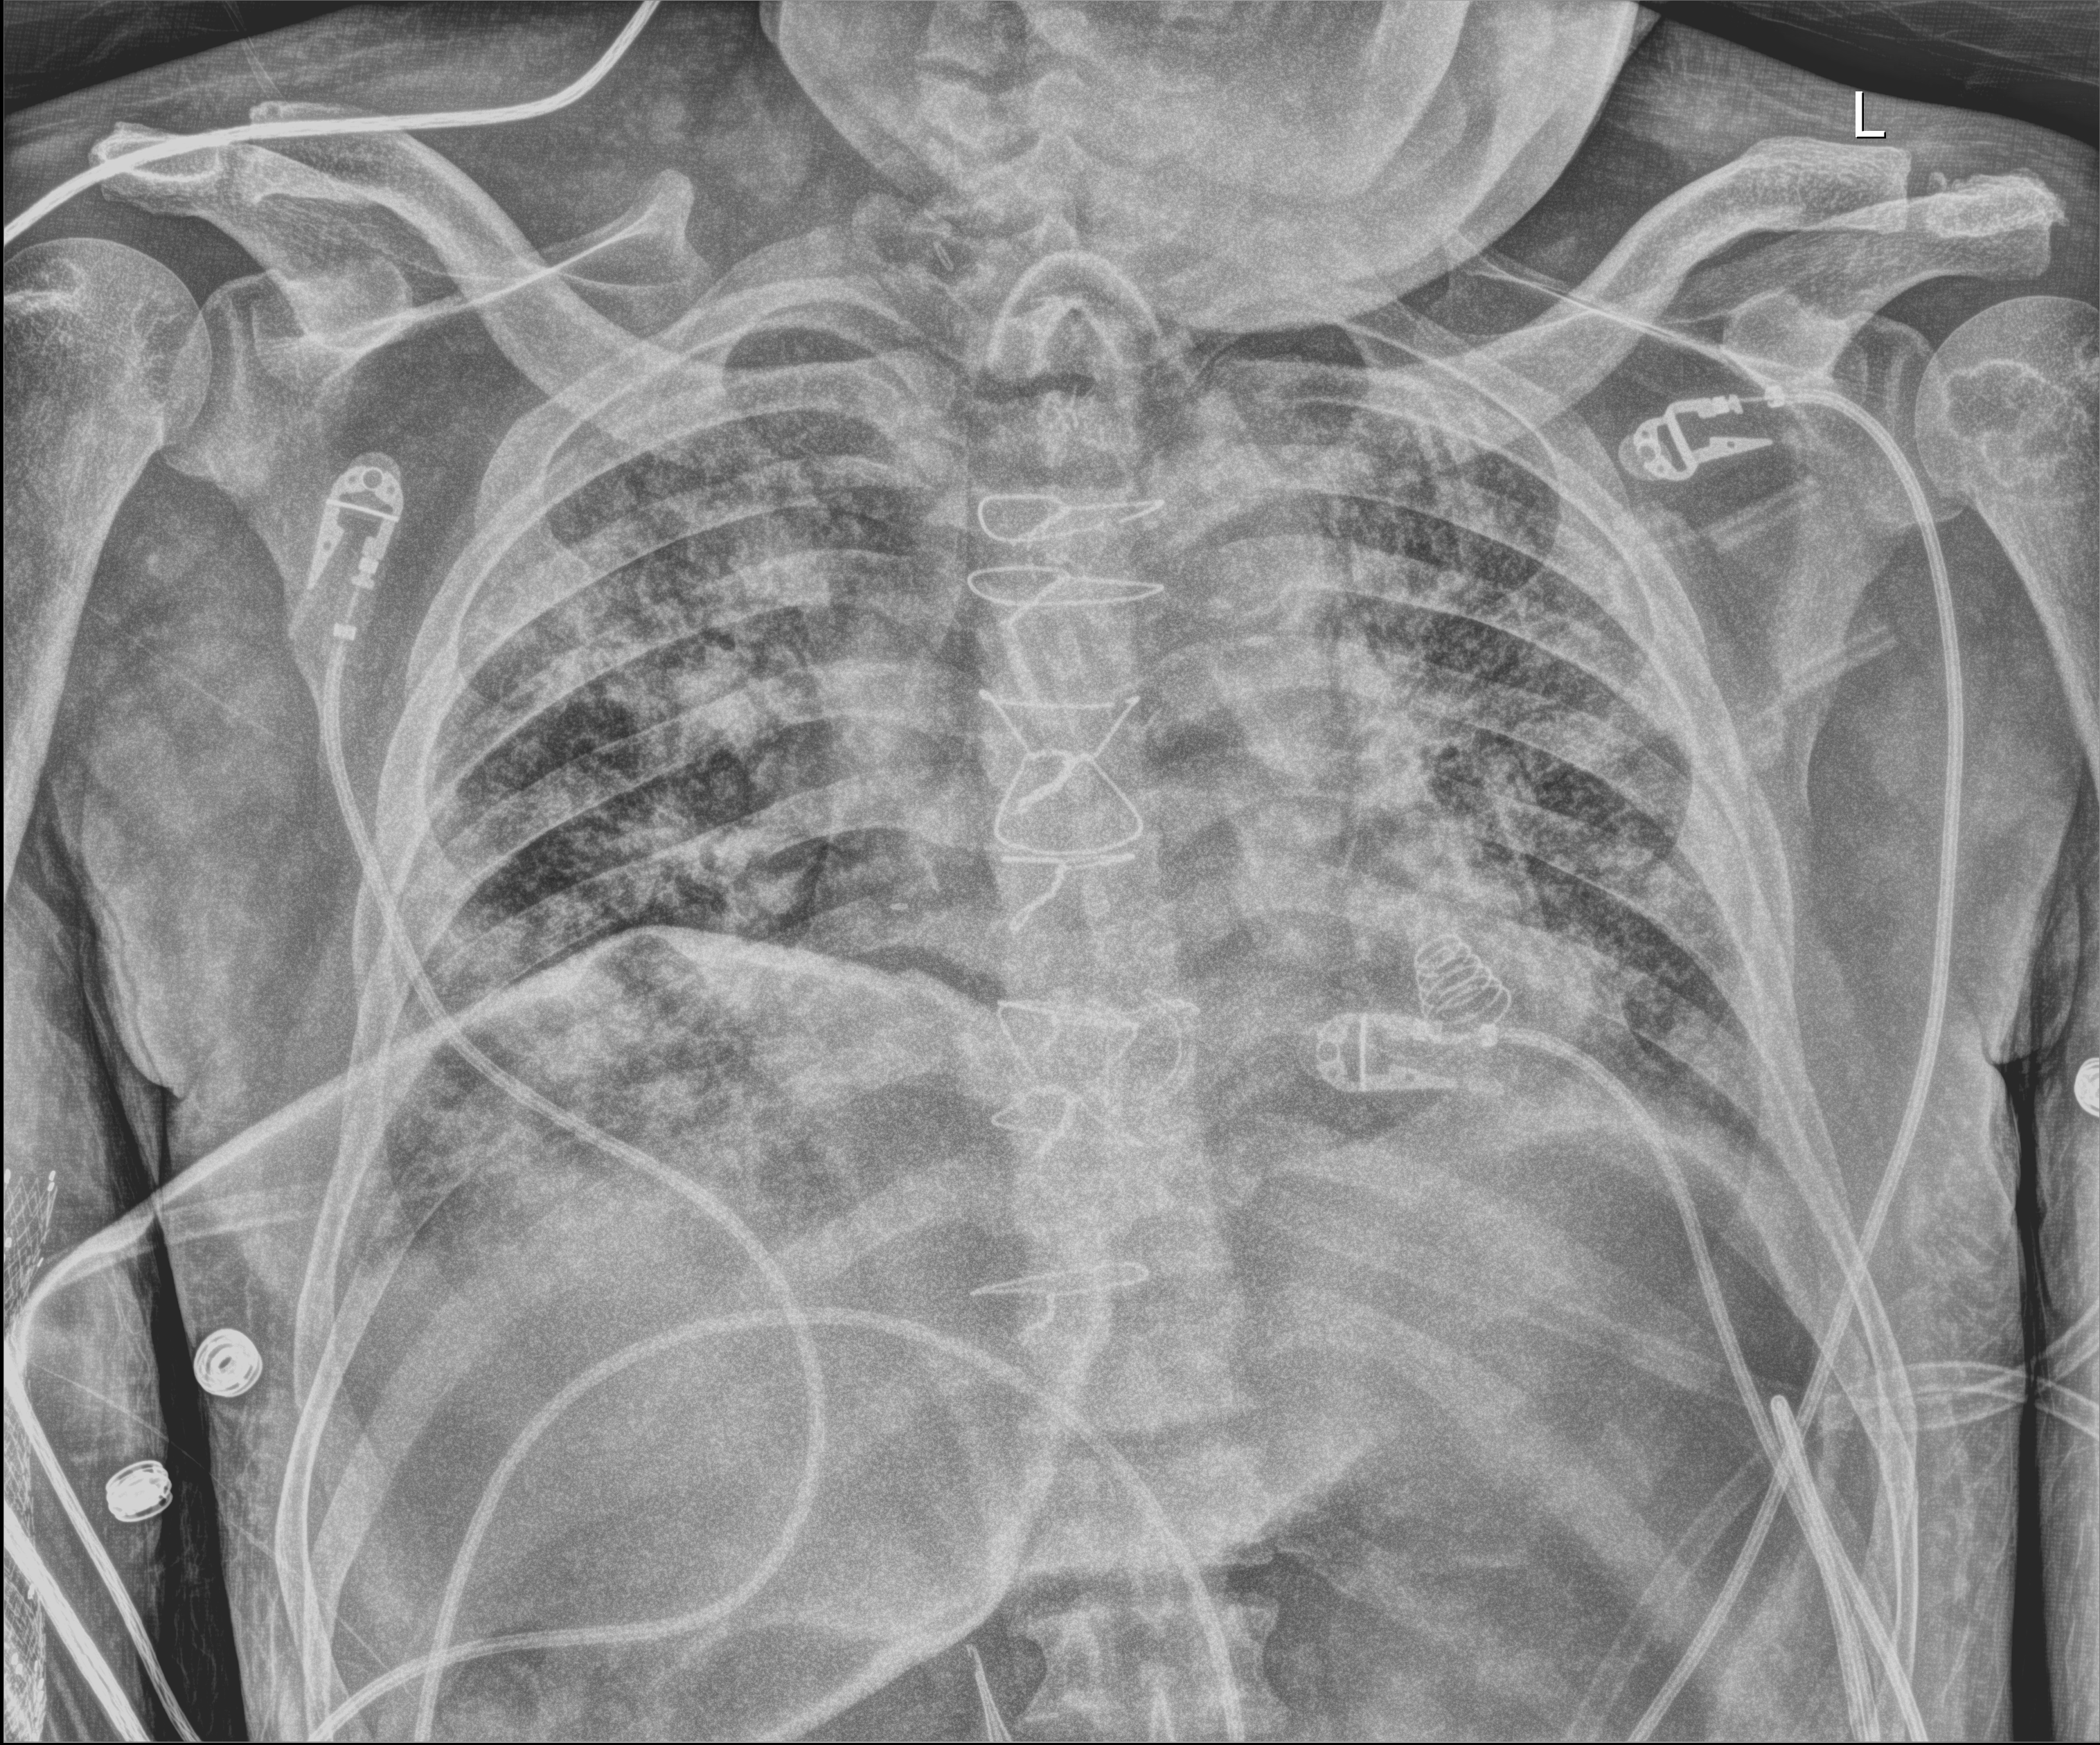
Chest X-ray (portable); anteroposterior (AP) projection. Male patient hospitalised with COVID-19, age 60–74 years.
Hospital-stay facts (about this admission, not read from this image; timing relative to this image not recorded): length of hospital stay: 50 days; mechanically ventilated during this hospital stay: yes.